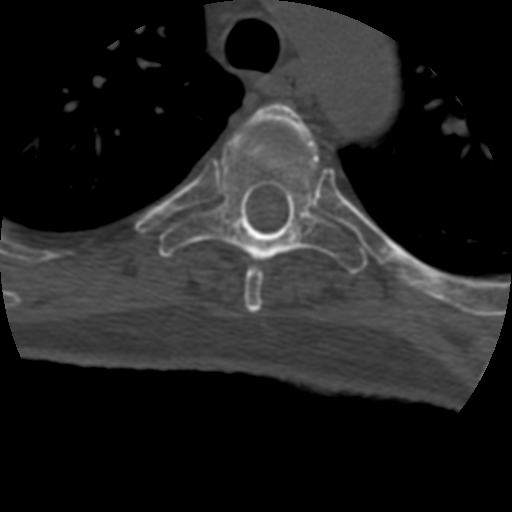
CT including the spine, one axial slice. Slice 323 of 399 in the series (ordered by position). Reconstruction kernel STANDARD. 120 kVp. Bone window (W 1800 / L 400 HU). 1.25 mm slice thickness. 512 × 512 image matrix. Patient age 69 years. From the clinical record (not read from this slice): primary cancer: prostate.
Annotated regions visible in this slice (semi-automatically segmented with operator editing):
- T4 vertebra: bounding box [x1, y1, x2, y2] px = [244, 102, 317, 313]
- T5 vertebra: [159, 120, 368, 274]